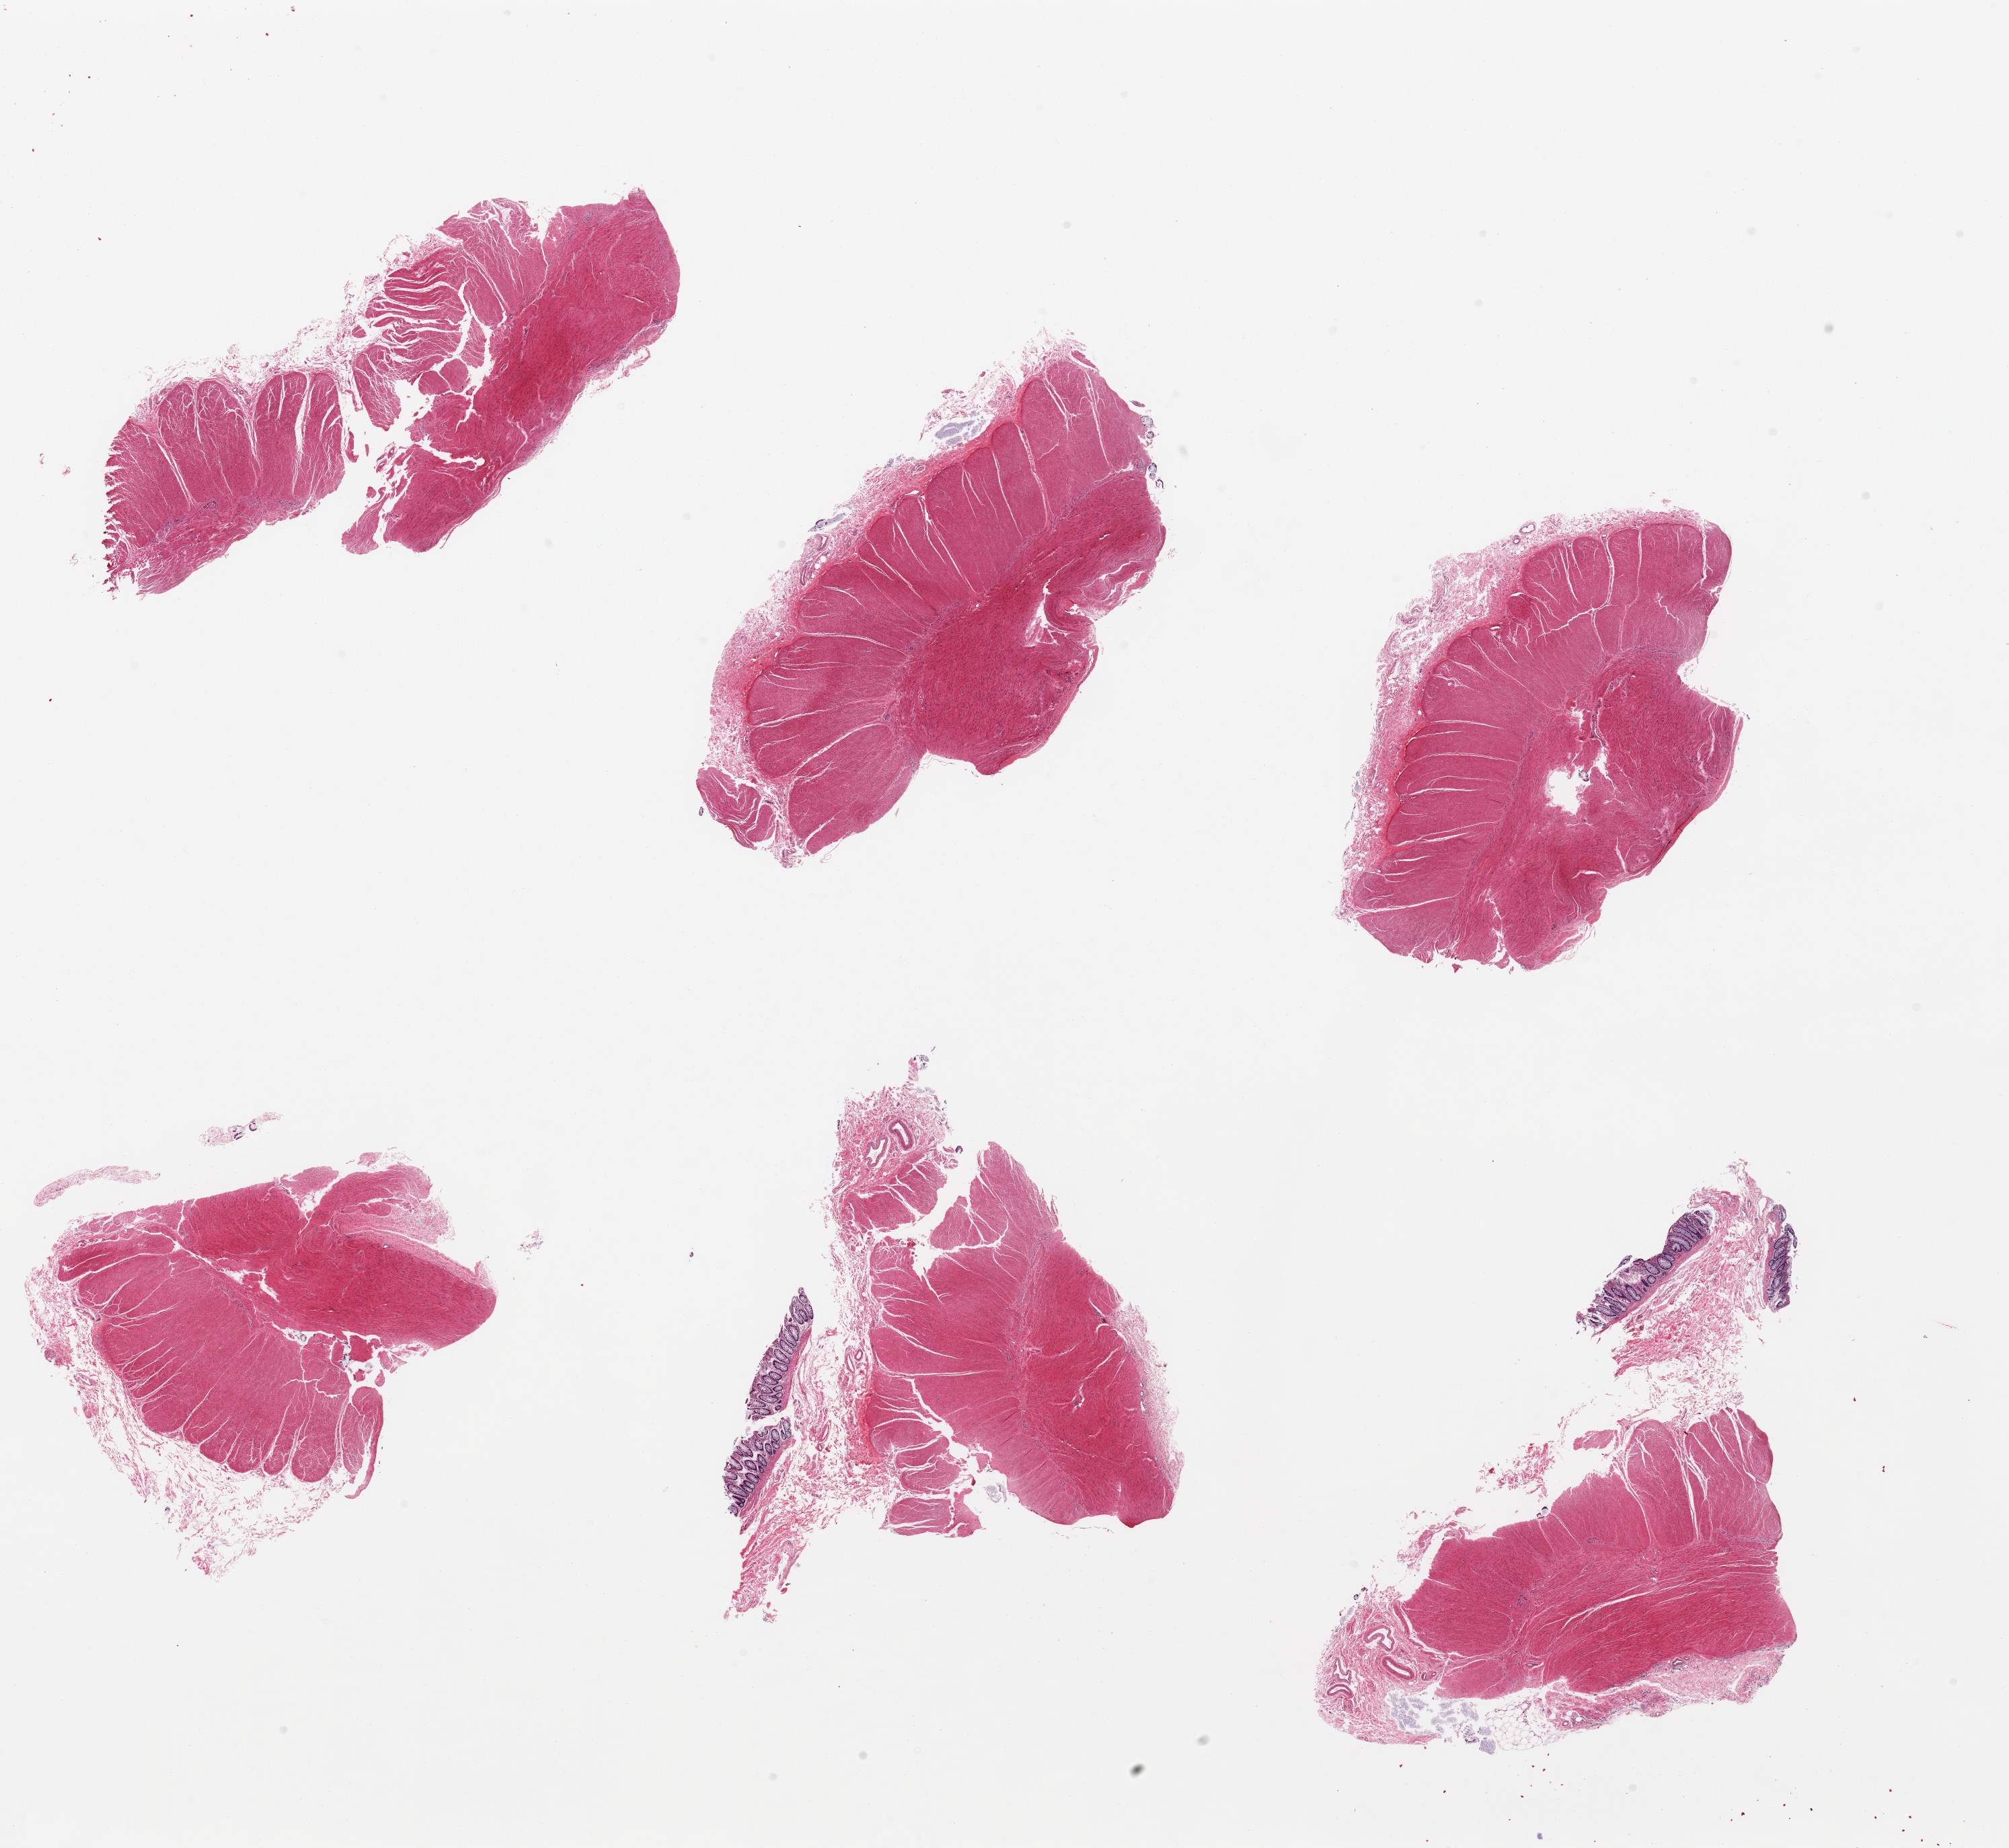
Digitized haematoxylin and eosin-stained section, whole scanned area (about 23.6 x 21.7 mm) shown as a low-resolution overview. PAXgene-fixed paraffin-embedded (PFPE) section. Target tissue: sigmoid colon. Donor tissue sample. Donor: female.
Reviewer comment on this tissue sample: 6 pieces, target muscularis, trace mucosa.